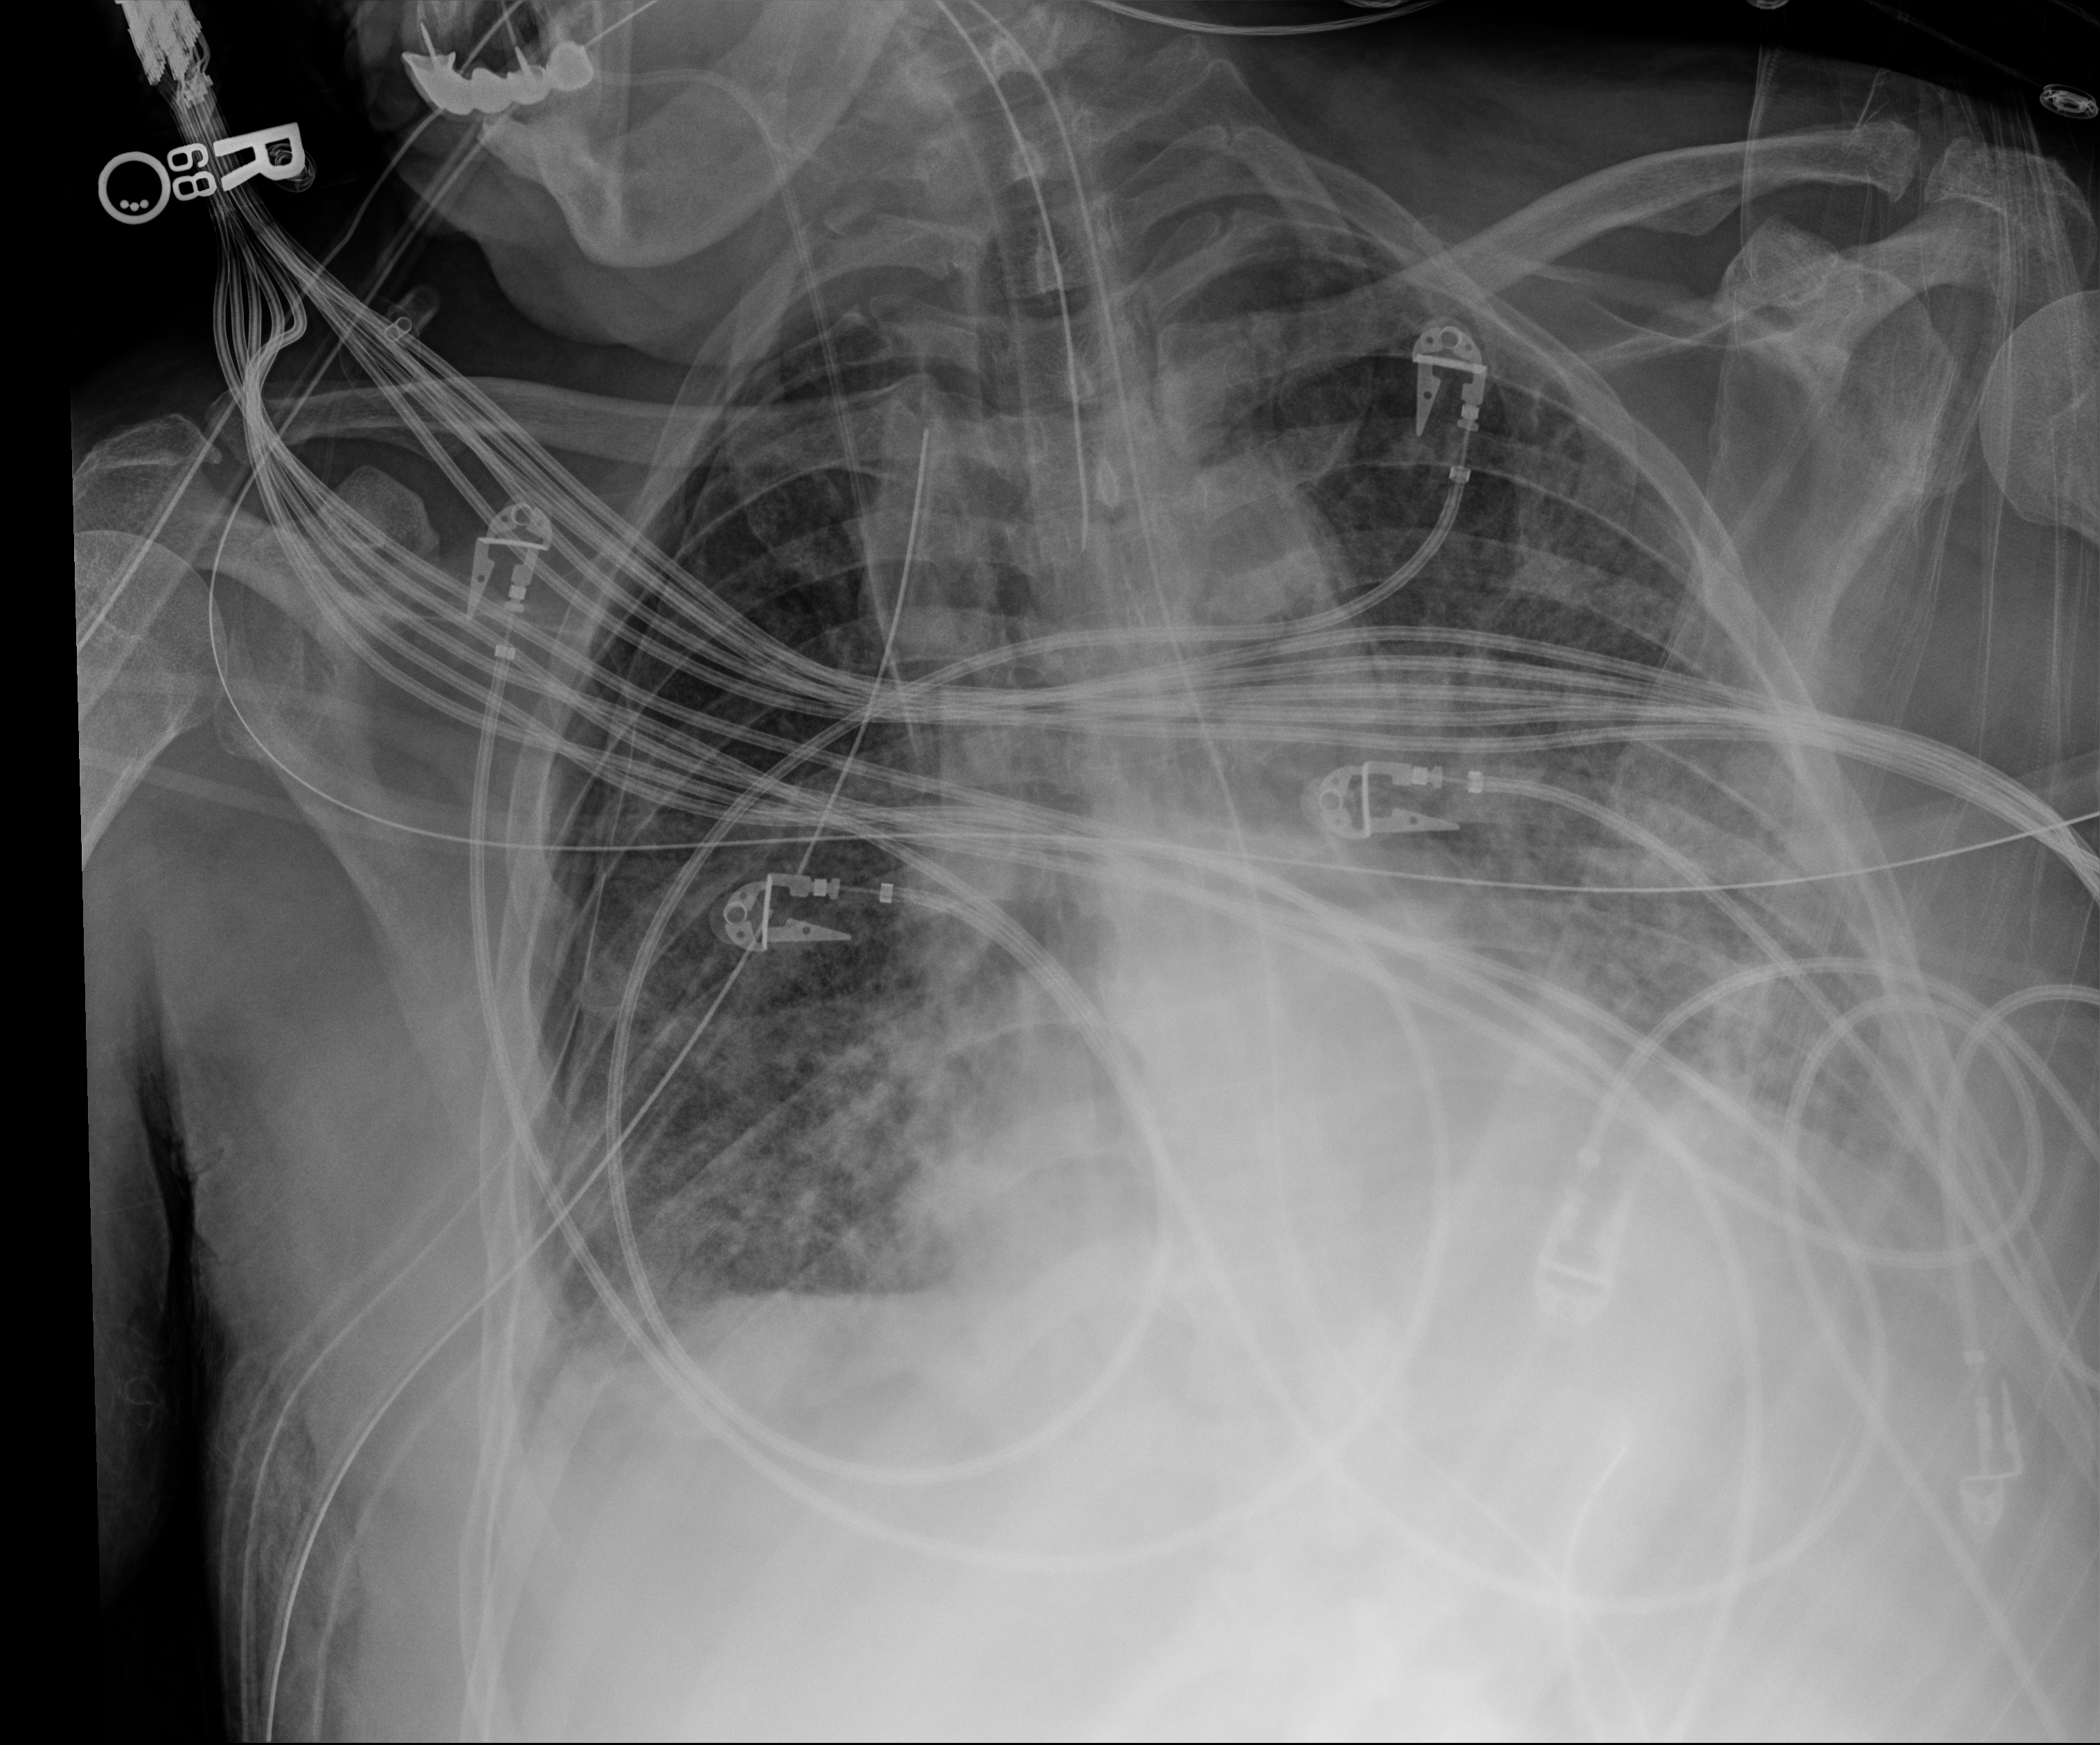
Bedside chest radiograph (digital radiography); anteroposterior (AP) projection. Male patient hospitalised with COVID-19, age 60–74 years.
From the hospital-stay record, not from the radiograph (when in the stay this image was taken is not recorded):
- admitted to intensive care during this hospital stay: yes
- other chronic lung disease (admission record): no